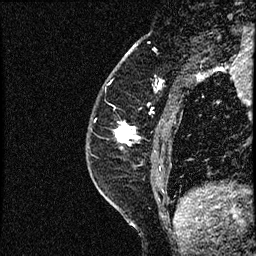
Breast MRI (dynamic contrast-enhanced), one sagittal slice. Position 18 of 52 along the scan axis. Dynamic contrast-enhanced study with each time point stored as its own series, time point 2 of 3 at this slice position (early post-contrast, ordered by acquisition time). 1.5 T. TE 4.2 ms, TR 17.6 ms. 256 × 256 image matrix. Patient: female, 49 years. From the clinical record (not read from this slice): setting: breast cancer imaged before/during neoadjuvant chemotherapy; receptor status: HER2-positive.
Structures marked on this image (semi-automatically segmented with operator editing):
- analysis volume of interest (the breast-tissue region the enhancement analysis was run in; not a lesion): bounding box (x1, y1, x2, y2) in pixels: (86, 65, 182, 175)
- tumour enhancement mask (voxels above the 100 % enhancement threshold inside the analysis volume of interest): (117, 124, 136, 145)